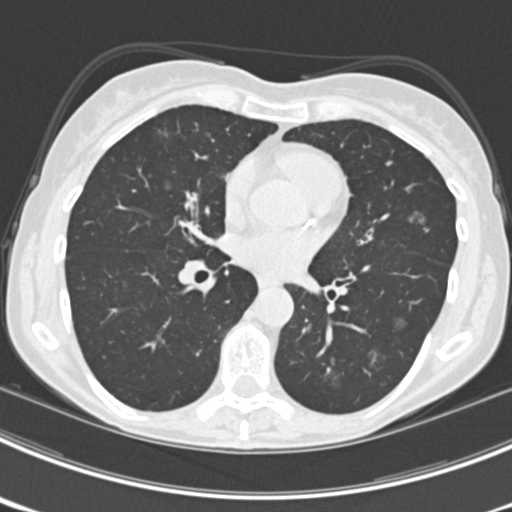
Low-dose screening chest CT, axial slice; third annual screen; lung window (W 1500 / L -600 HU); 2 mm slice thickness; standard (soft-tissue) reconstruction kernel (B30f); 120 kVp. Female, age 63 years at enrolment. Current smoker at enrolment.
- Lesion marked by an expert reader, bounding box [x1, y1, x2, y2] px = [405, 200, 443, 236].
- The screening reader recorded 9 non-calcified nodules or masses ≥4 mm on this exam (left upper lobe, right upper lobe, left upper lobe, left lower lobe, right middle lobe, left lower lobe, left lower lobe, right lower lobe, right lower lobe); which of them this box marks is not recorded.
- Lung cancer was diagnosed 15 days after this screen: bronchiolo-alveolar adenocarcinoma, NOS, right upper lobe, right middle lobe, right lower lobe, left upper lobe, left lower lobe, moderately differentiated (G2), stage IV (AJCC 6th edition).